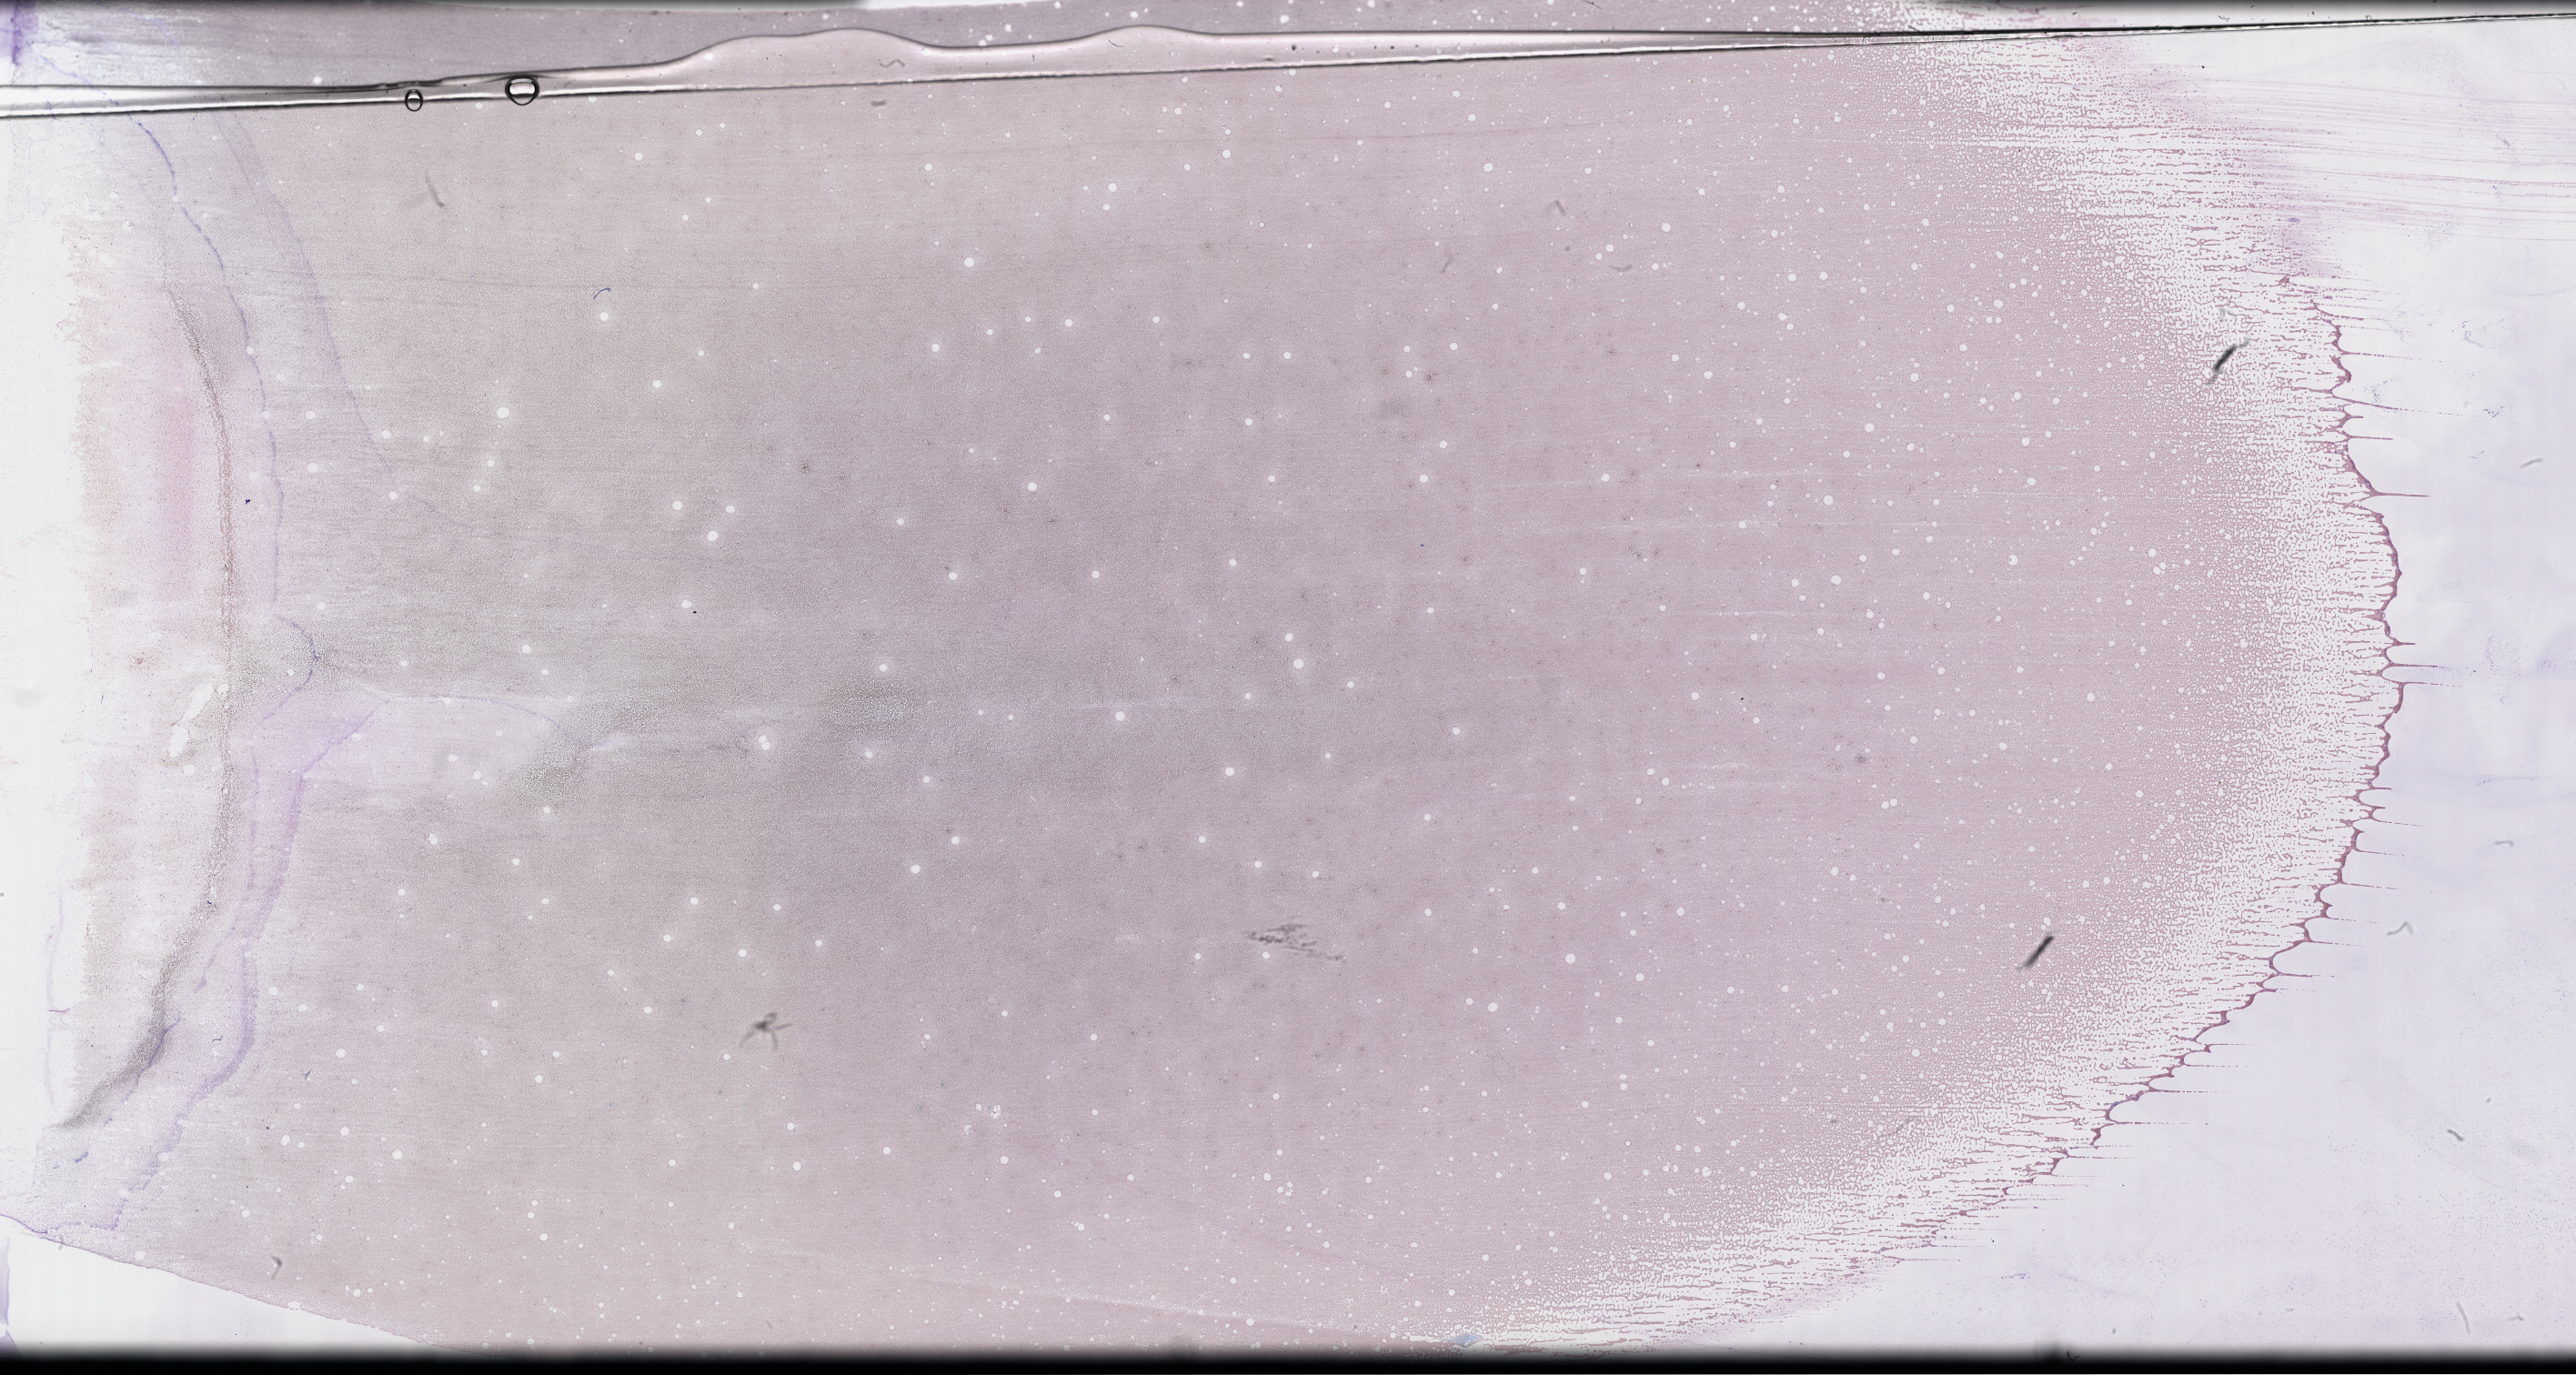
Whole-slide image of a whole blood smear, Wright–Giemsa stain, low-resolution overview of the scanned area, about 45.7 x 24.4 mm; smear from an EDTA sample; specimen time point: collected on treatment. Male patient.
From a patient with: Plasma Cell Myeloma.